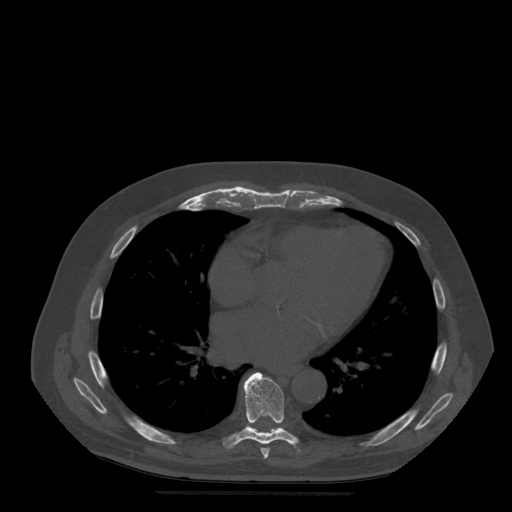
CT including the spine, one axial slice; slice 312 of 522 in the series (ordered by position); bone window (W 1800 / L 400 HU); 512 × 512 image matrix, field of view 420 × 420 mm. Patient age 72 years. From the clinical record (not read from this slice): primary cancer: prostate.
Structures marked on this image (semi-automatically segmented with operator editing):
- T7 vertebra: bounding box <261,448,270,459> (left, top, right, bottom; pixels)
- T8 vertebra: <223,372,300,451>